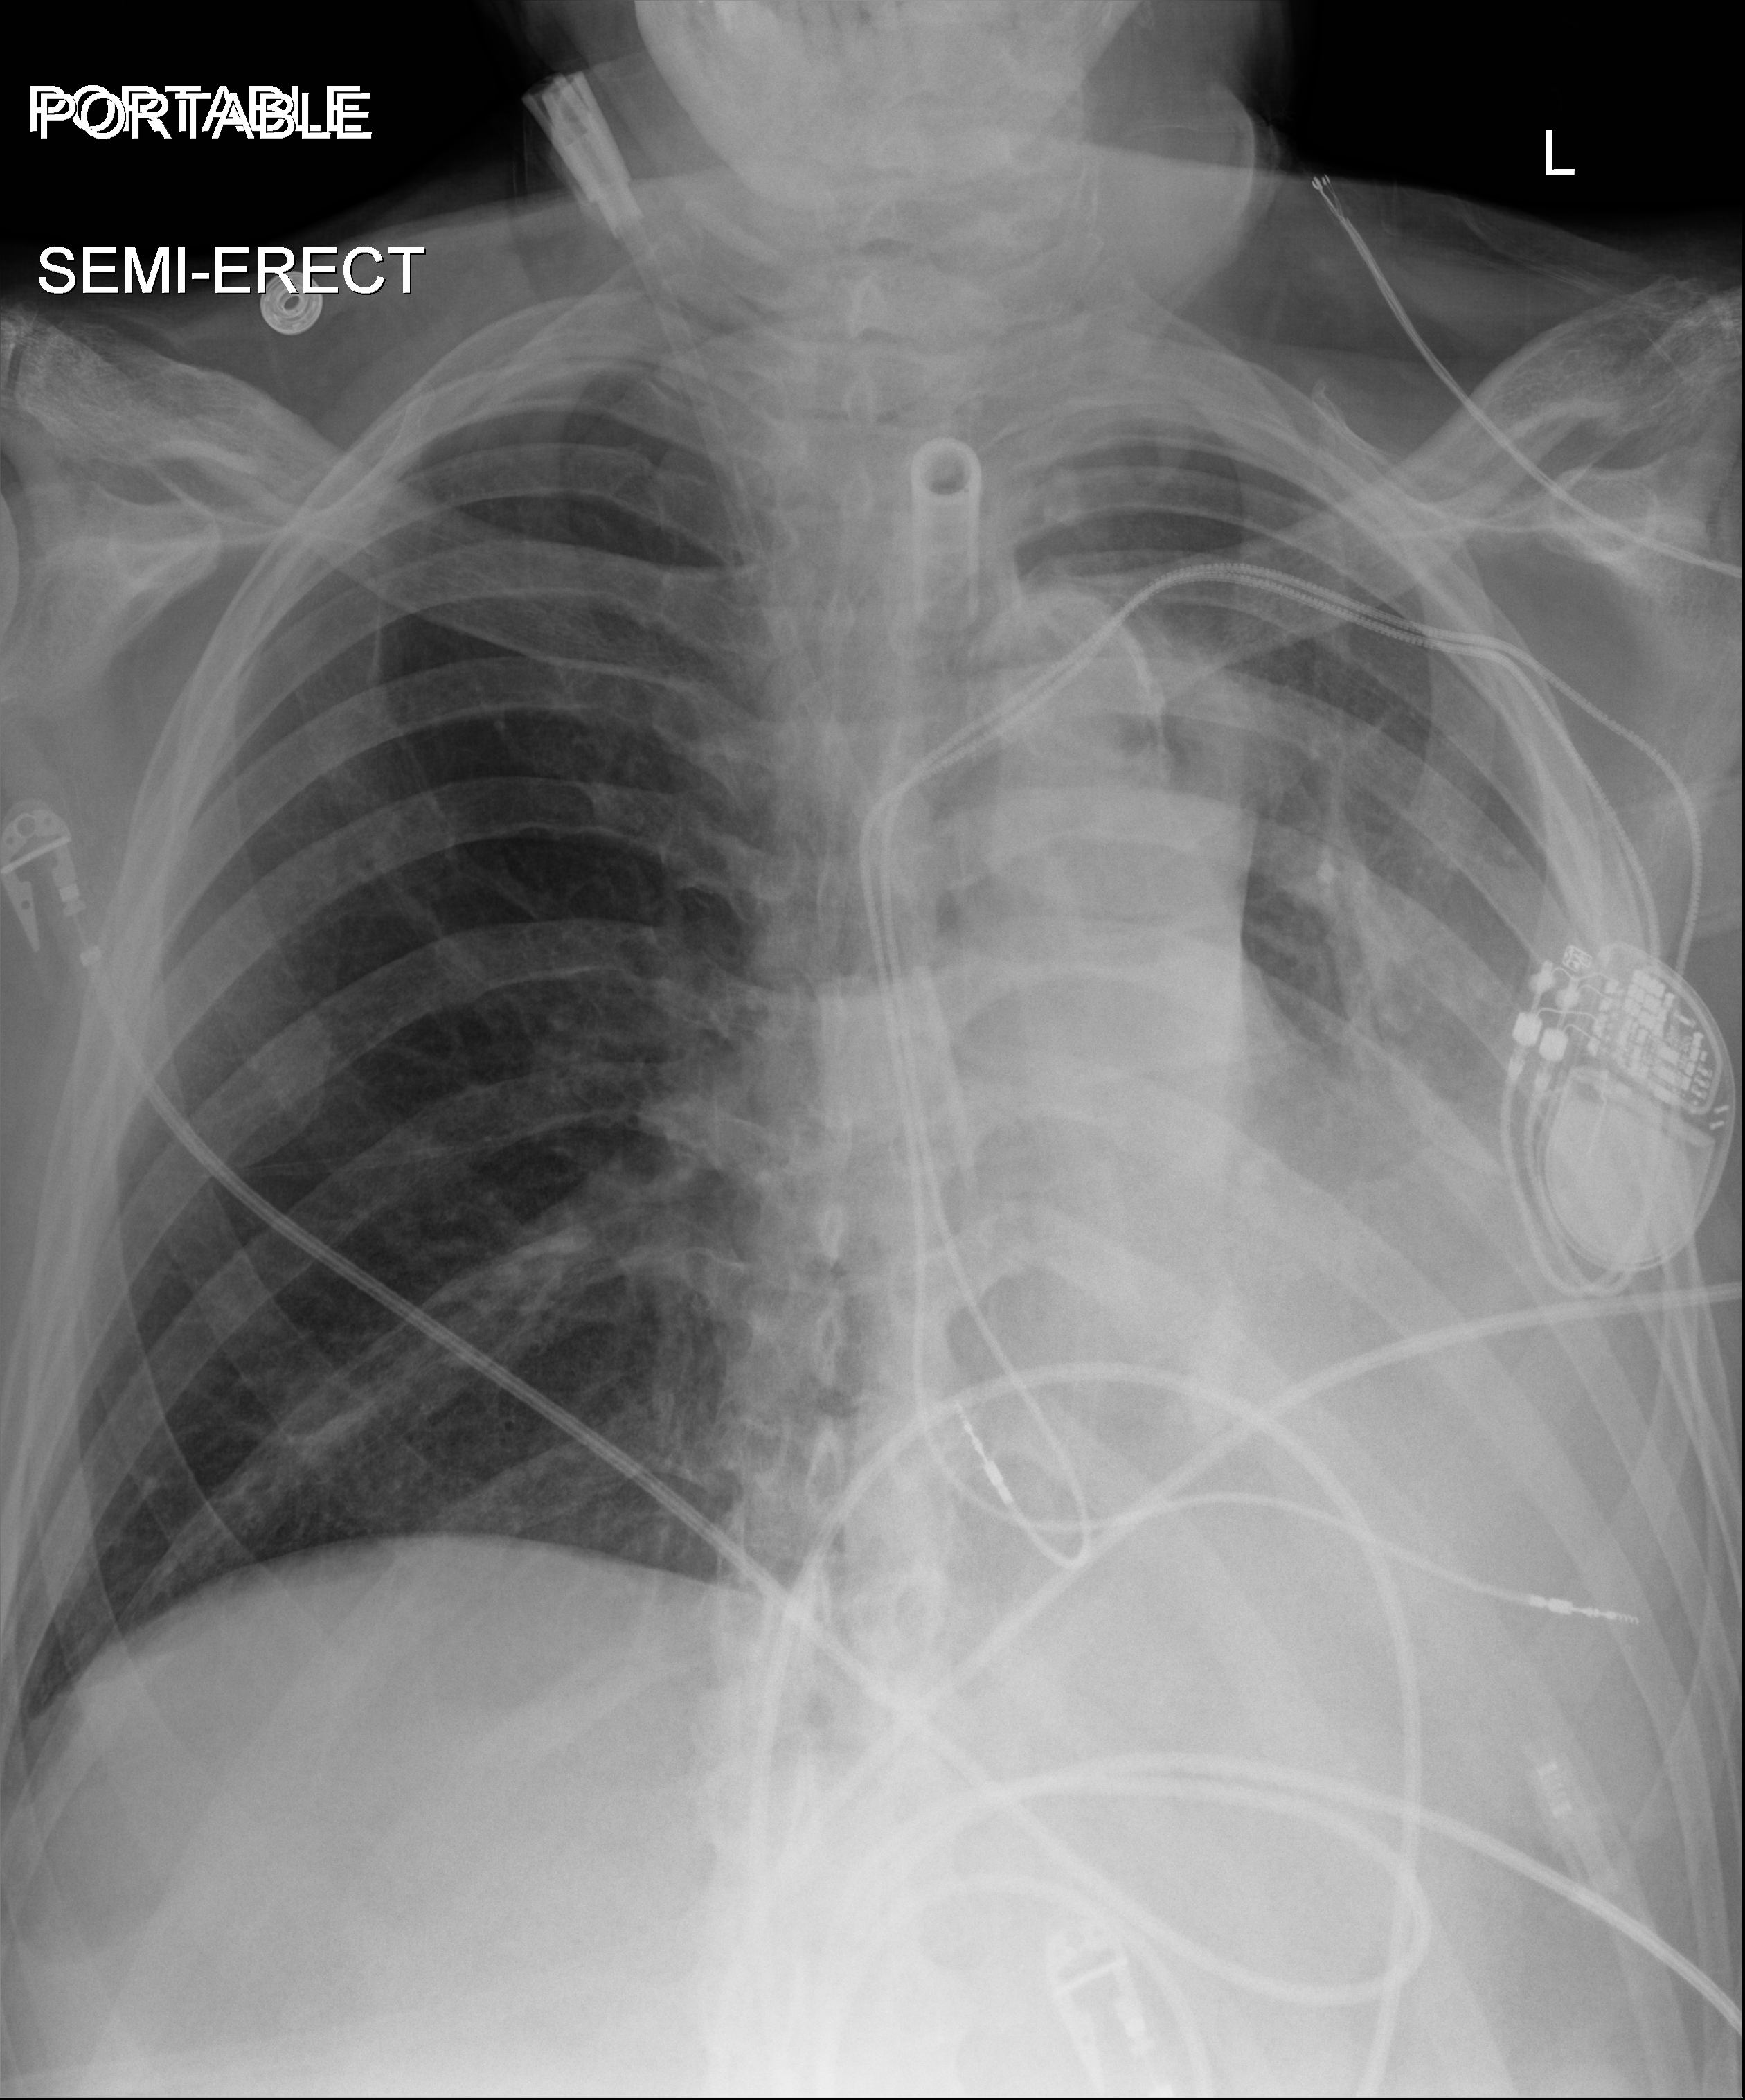
Bedside chest radiograph (digital radiography); anteroposterior (AP) projection. Male patient hospitalised with COVID-19, age 60–74 years.
Admission-level facts for this patient (not findings on this image; timing relative to this image not recorded):
- length of hospital stay: 41 days
- admitted to intensive care during this hospital stay: yes